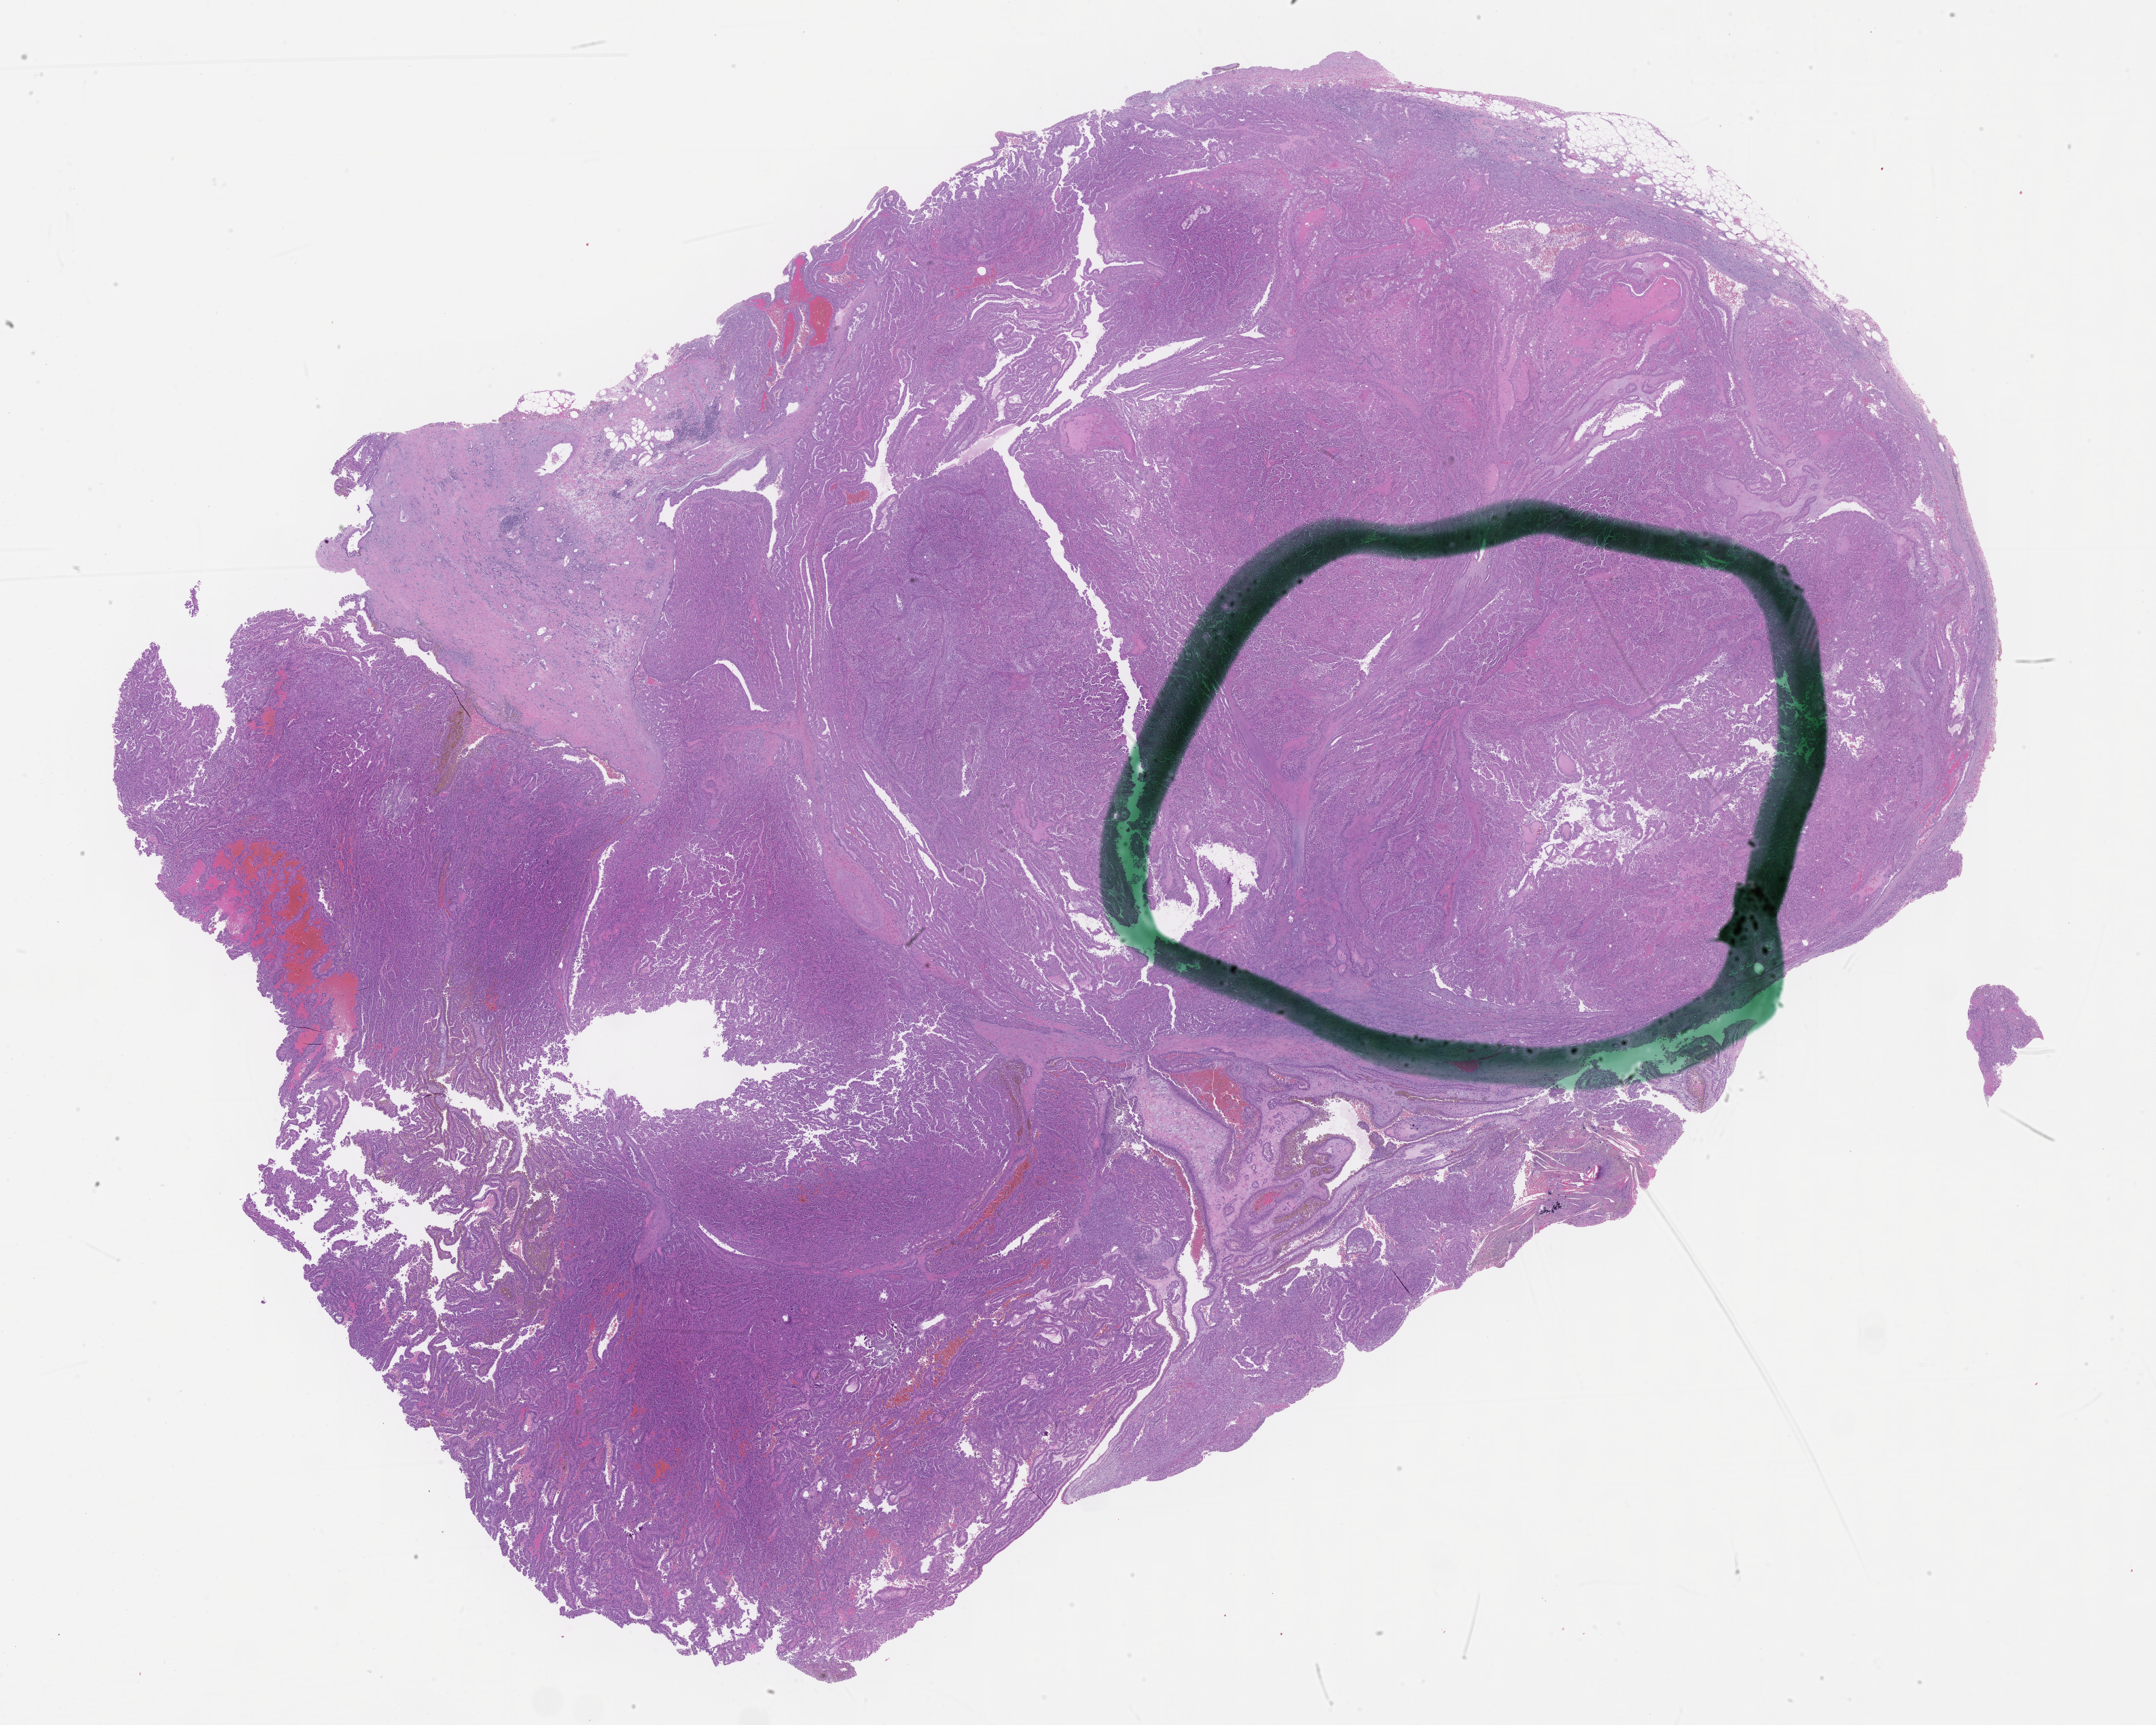
Digitized H&E tissue section (whole slide), whole scanned area (about 25.7 x 20.5 mm, slide scanned at 40x) shown as a low-resolution overview; FFPE section; primary tumour sample from the kidney. Patient: male, age at initial diagnosis 74 years.
* AJCC pathologic stage: III (7th edition)
* pathologic diagnosis: Papillary adenocarcinoma, NOS
* lymph nodes positive (case pathology): 5 of 7 examined